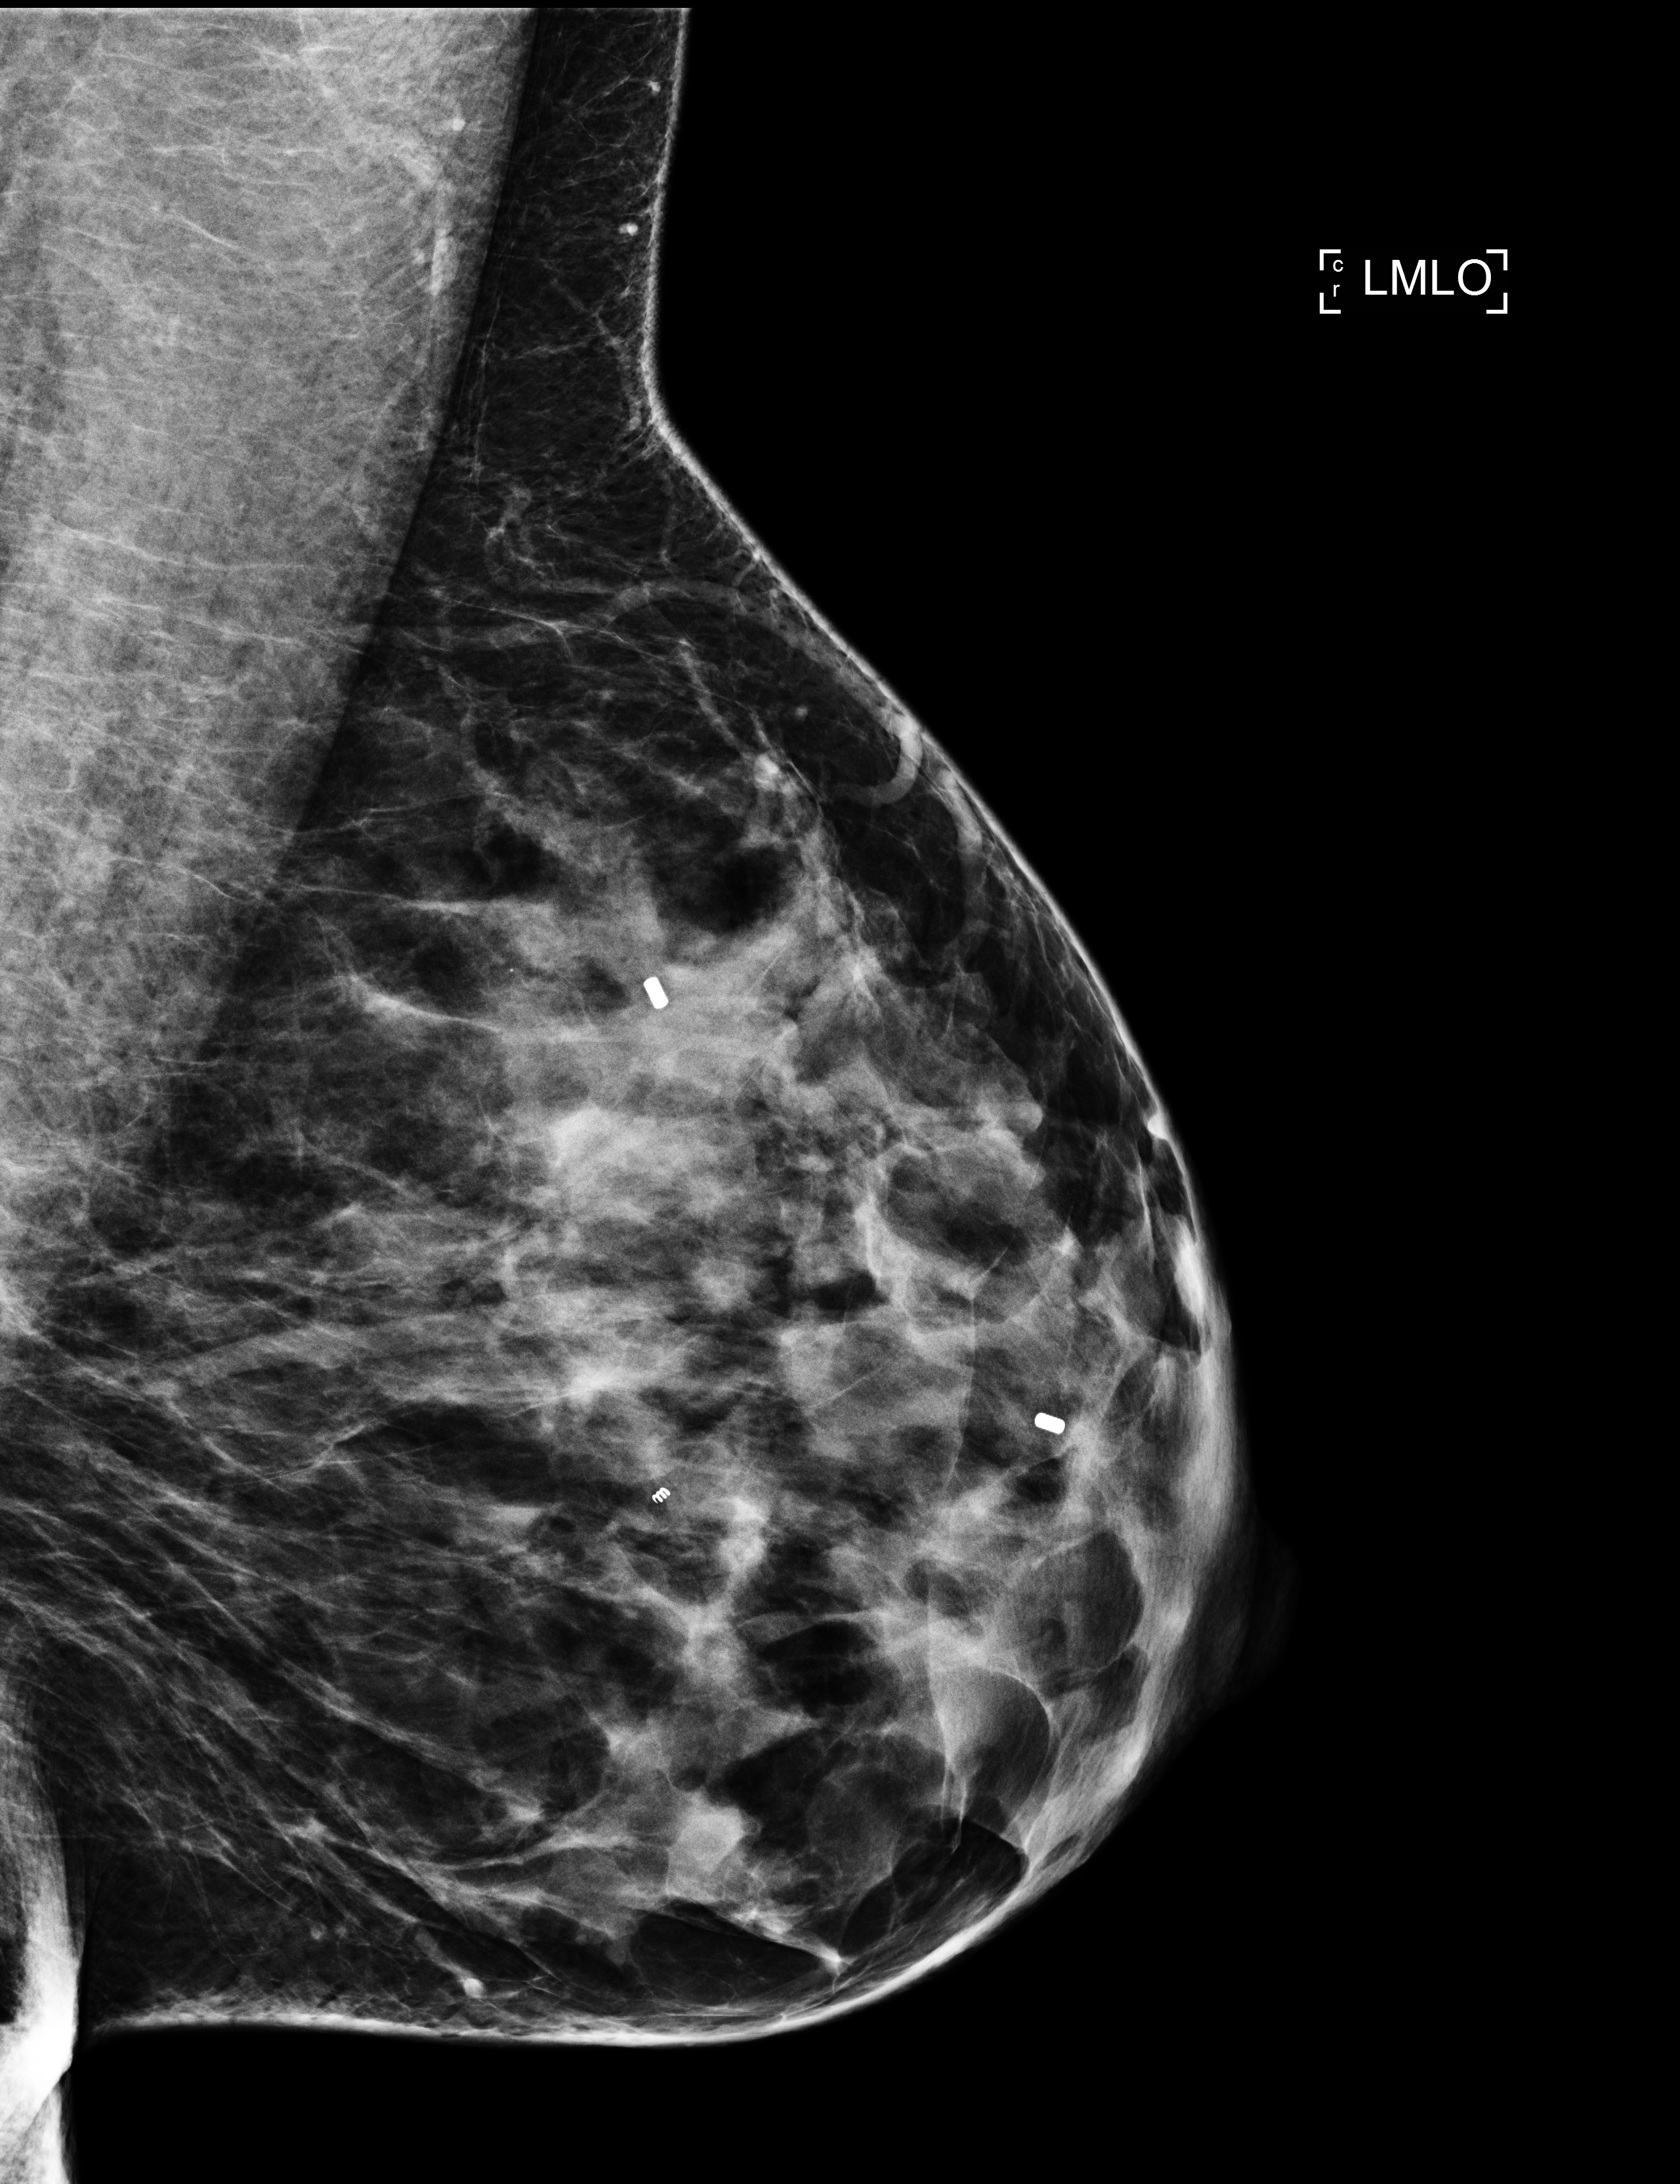
Screening examination, system: Selenia Dimensions. Female patient, age 49 years.
Image type: full-field digital mammogram. Breast: left. Projection: mediolateral oblique (MLO) view.